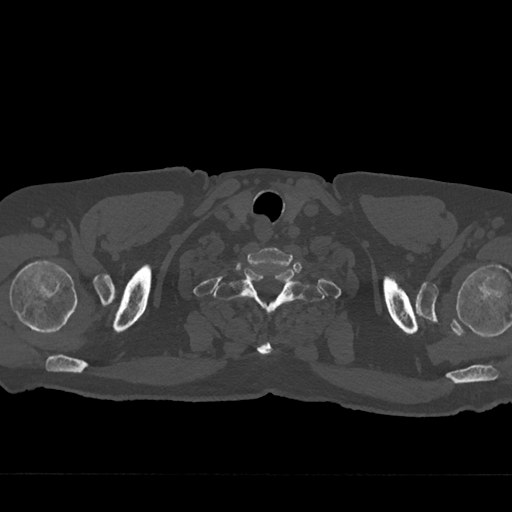
CT including the spine, one axial slice. 120 kVp. Bone window (W 1800 / L 400 HU). 0.5 mm slice thickness. 512 × 512 image matrix. Patient: male, 75 years. Case-level facts recorded for this patient, not image findings: primary cancer: renal; vertebrae with lytic lesions (as recorded): T4.
Structures marked on this image (semi-automatic segmentation, software-assisted and operator-edited):
- T1 vertebra: box from (x=214, y=268) to (x=324, y=355) px